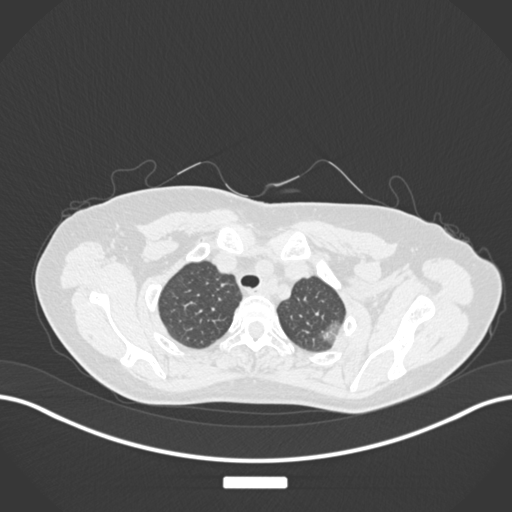
Chest CT, one axial slice; position 149 of 181 along the scan axis; reconstruction kernel B30f; lung window (W 1500 / L -600 HU); 512 × 512 image matrix, field of view 400 × 400 mm. Patient: female, 58 years. Case-level facts recorded for this patient, not image findings: clinical TNM (as recorded): T1c N0 M0.
Structures marked on this image (rectangle marked by the reading radiologist):
- lung tumour (recorded histology: adenocarcinoma): bounding box <316,316,345,346> (left, top, right, bottom; pixels)